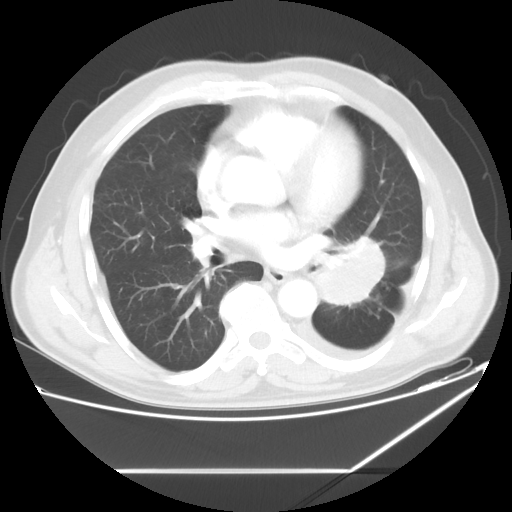
Chest CT, one axial slice. Position 30 of 60 along the scan axis. Reconstruction kernel STANDARD. 120 kVp. Lung window (W 1500 / L -600 HU). 512 × 512 image matrix. Patient: male, 62 years. From the clinical record (not read from this slice): clinical TNM (as recorded): T3 N0 M1.
Annotated regions visible in this slice (bounding box drawn by a radiologist):
- lung tumour (recorded histology: adenocarcinoma): bounding box [x1, y1, x2, y2] px = [313, 234, 385, 310]
- lung tumour (recorded histology: adenocarcinoma): [318, 239, 386, 307]